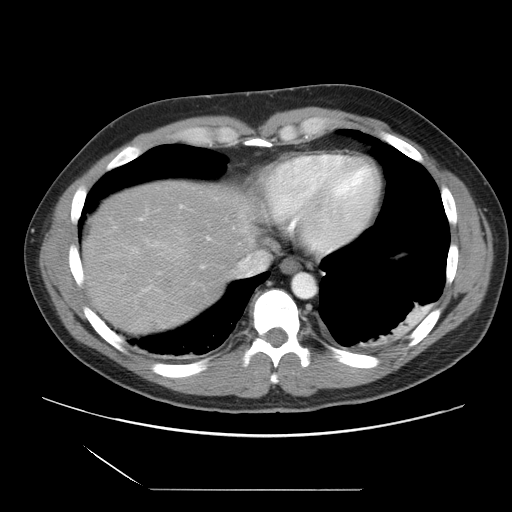
Contrast-enhanced abdominal CT, one axial slice. Slice 29 of 39 in the series (ordered by position). Intravenous contrast given. Soft-tissue window (W 400 / L 40 HU). 5 mm slice thickness. 512 × 512 image matrix. Male patient, age 39 years. From the clinical record (not read from this slice): diagnosis: colorectal cancer liver metastases, imaged before liver resection.
Outlined on this slice (outlined manually by an expert reader):
- hepatic veins: bounding box <234,253,258,276> (left, top, right, bottom; pixels)
- liver: <82,181,258,337>
- planned liver remnant (the part of the liver to remain after resection): <142,181,258,250>
- portal vein (with intrahepatic branches): <132,206,182,292>
- liver metastasis: <161,277,173,290>